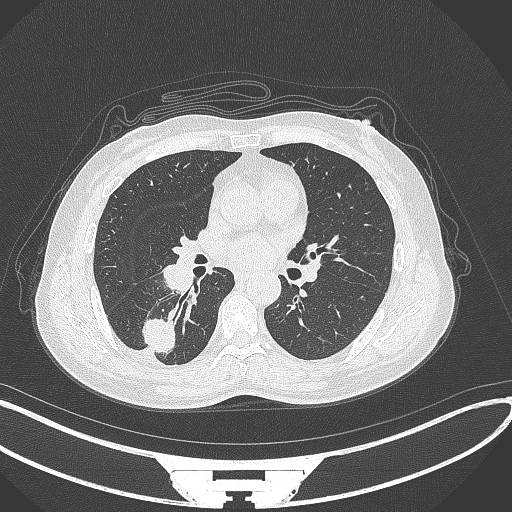
Chest CT, one axial slice; position 157 of 352 along the scan axis; reconstruction kernel B70f; 120 kVp; lung window (W 1500 / L -600 HU); 1 mm slice thickness; 512 × 512 image matrix, field of view 400 × 400 mm. Female patient, age 55 years. Case-level facts recorded for this patient, not image findings: clinical TNM (as recorded): T1c N1 M0.
Annotated regions visible in this slice (bounding box drawn by a radiologist):
- lung tumour (recorded histology: adenocarcinoma): bounding box [x1, y1, x2, y2] px = [140, 318, 178, 354]